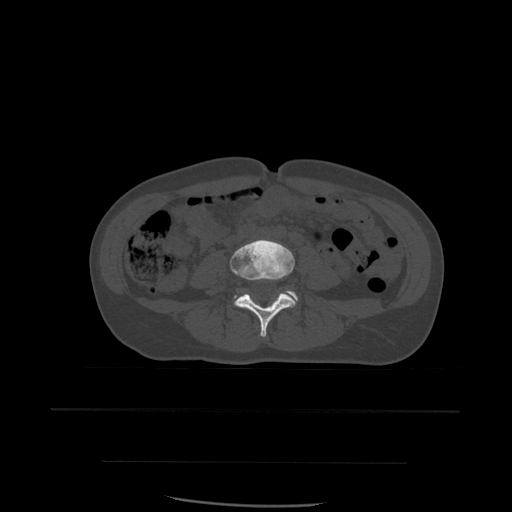
CT including the spine, one axial slice. Position 166 of 574 along the scan axis. Bone window (W 1800 / L 400 HU). 1.25 mm slice thickness. 512 × 512 image matrix. Patient age 48 years. Case-level facts recorded for this patient, not image findings: primary cancer: lung.
Structures marked on this image (semi-automatically segmented with operator editing):
- L4 vertebra: bounding box <230,240,296,338> (left, top, right, bottom; pixels)
- L5 vertebra: <235,291,298,307>